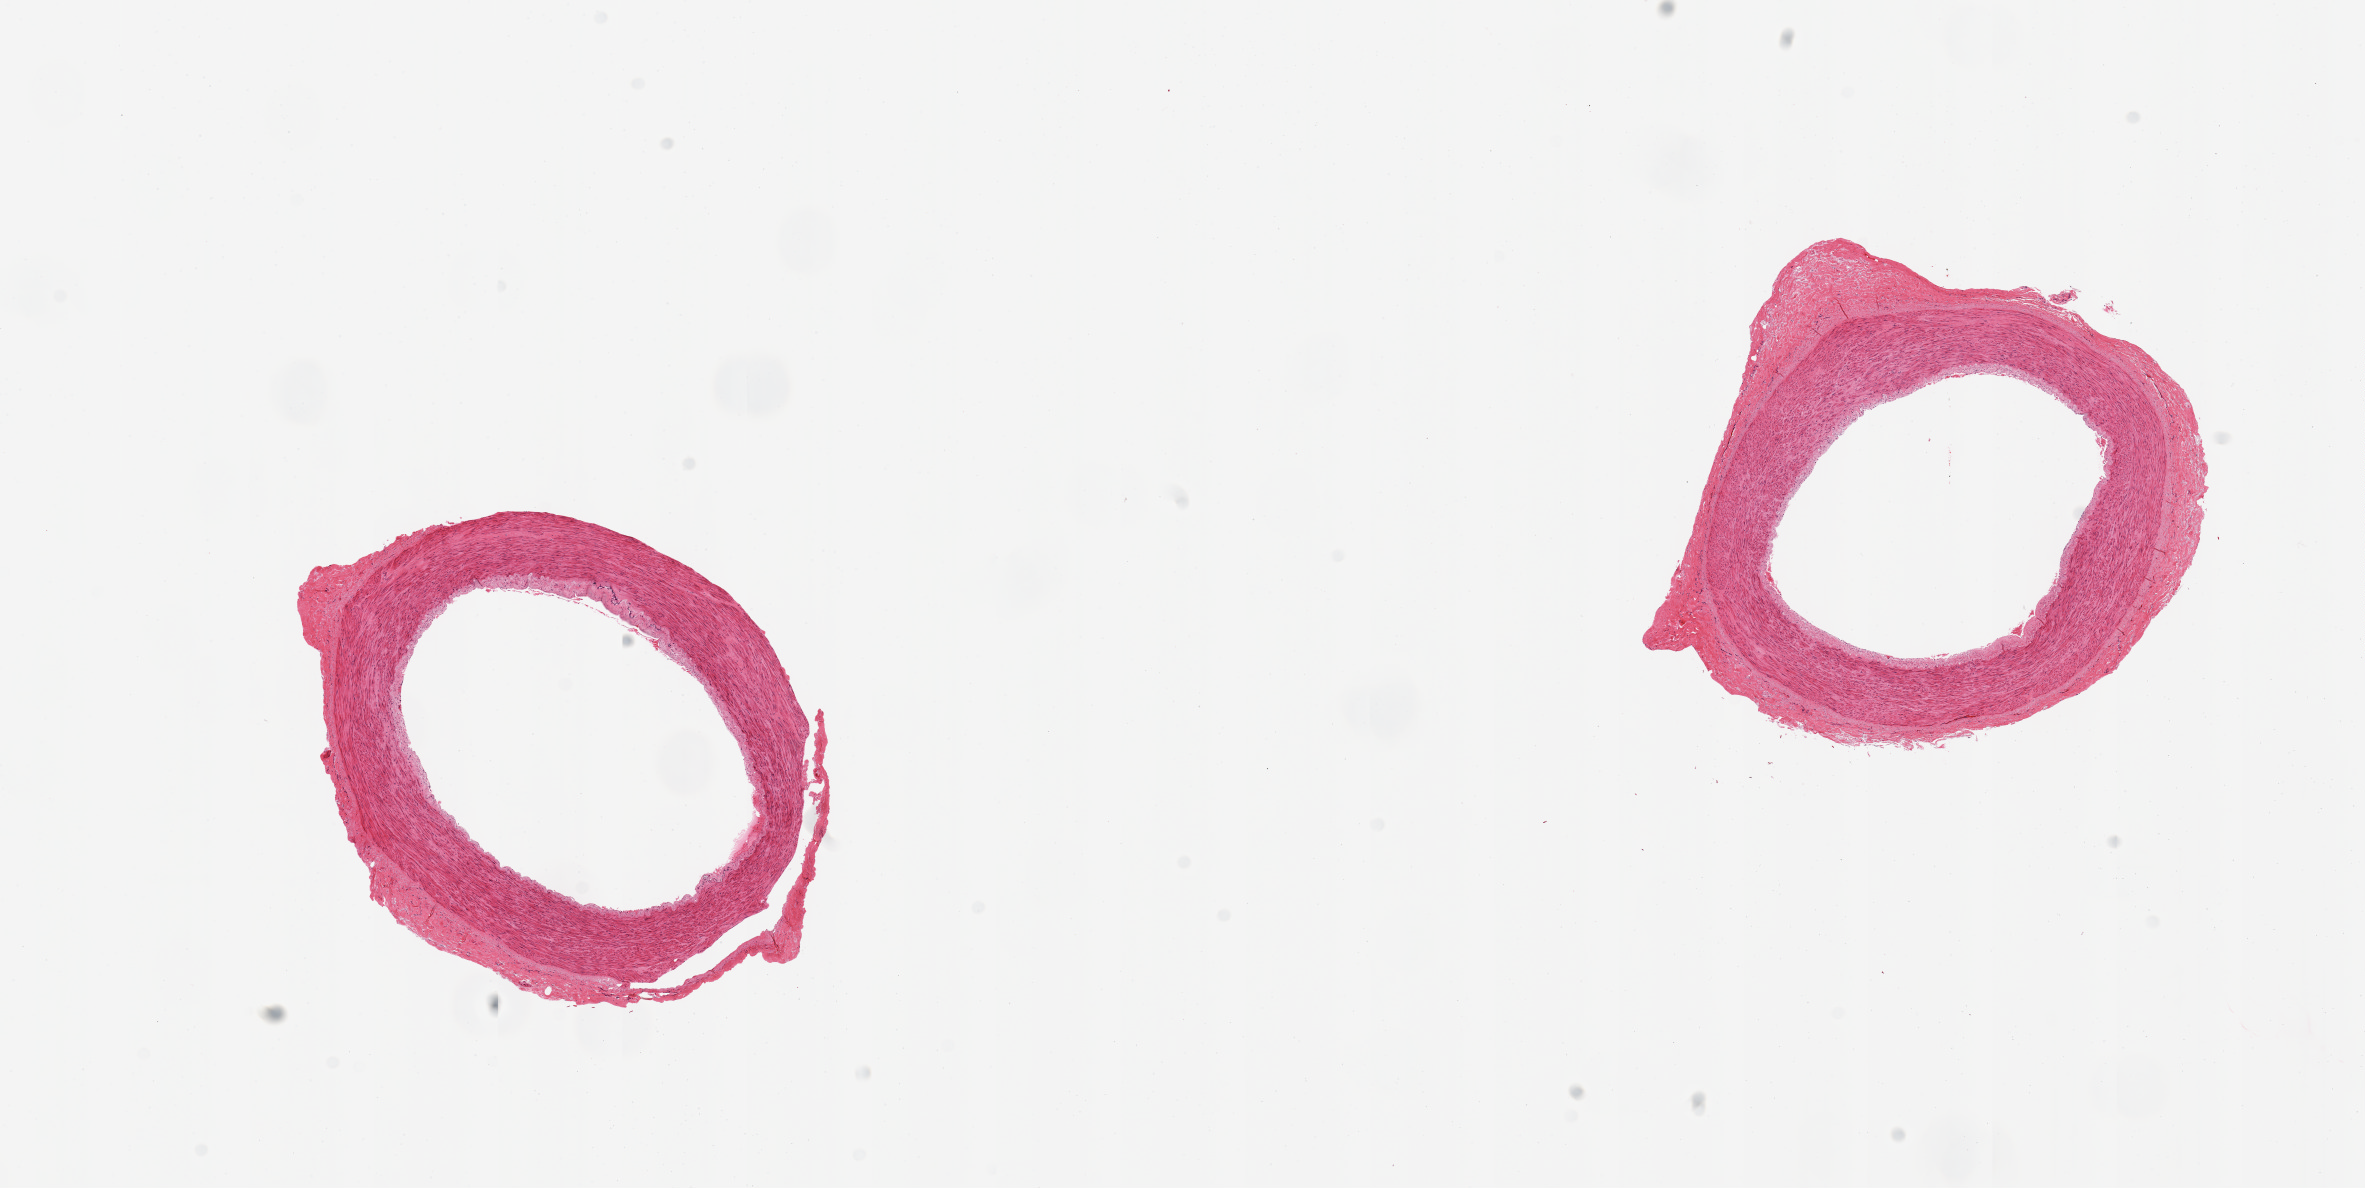
Whole-slide image, H&E stain, a low-resolution overview of the entire scanned area, about 18.7 x 9.4 mm. PAXgene-fixed paraffin-embedded (PFPE) section. Target tissue: tibial artery. Donor tissue sample. Donor: female.
- review note (as recorded): 2 pieces; no lesions